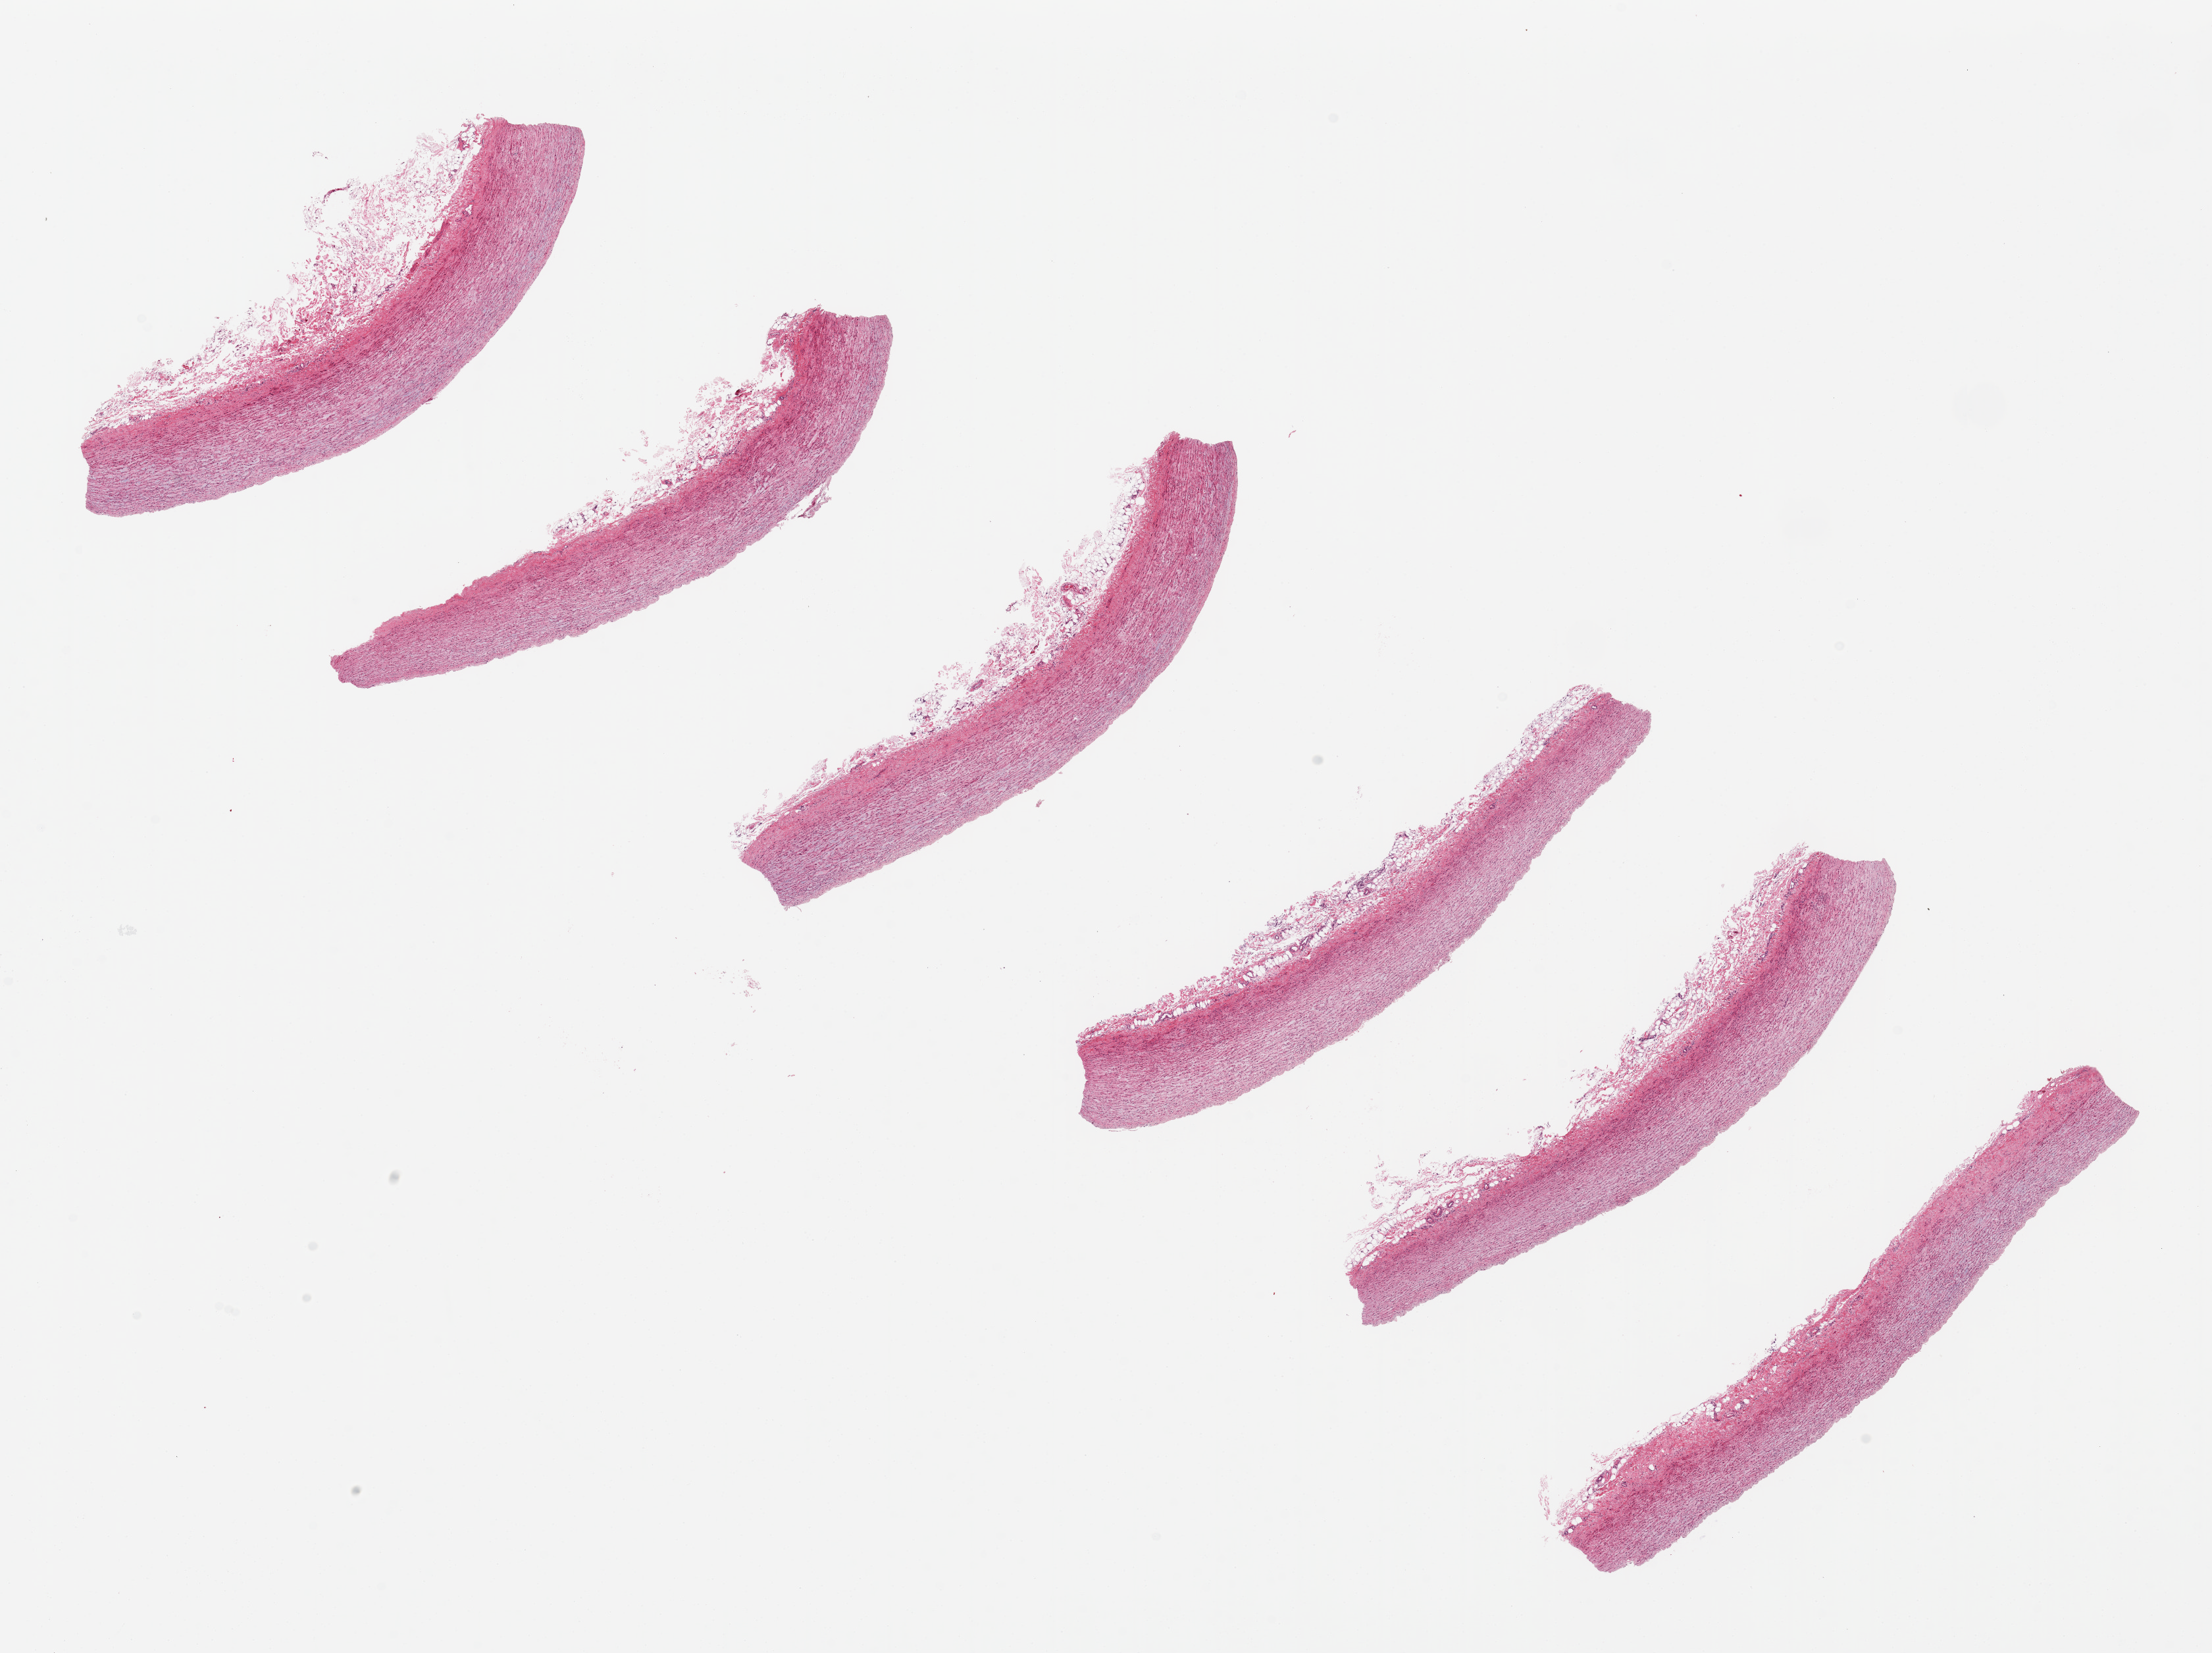
H&E whole-slide image, shown as a low-resolution overview of the whole scanned area (about 26.6 x 19.9 mm), PAXgene-fixed paraffin-embedded (PFPE) section, section of aorta (target tissue), donor tissue sample.
Pathologist's review note for this sample: 6 ~7x1mm pieces.